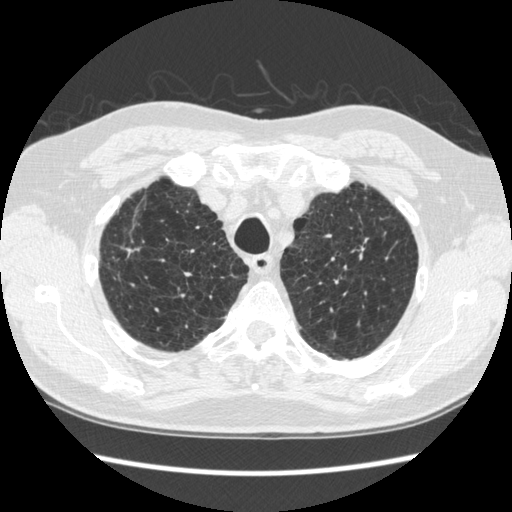
Axial slice from a low-dose chest CT screening exam. Second screening round (one year after baseline). Lung window (W 1500 / L -600 HU). 1.25 mm slice thickness. 120 kVp. 512 × 512 image matrix. Male, age 70 years at enrolment. Former smoker at enrolment.
- Lesion marked by an expert reader, bounding box <334,212,394,279> (left, top, right, bottom; pixels).
- The screening reader recorded 5 non-calcified nodules or masses ≥4 mm on this exam (right lower lobe, right lower lobe, right lower lobe, left upper lobe, left lower lobe); which of them this box marks is not recorded.
- Participant outcome: lung cancer diagnosed 479 days after this screen — squamous cell carcinoma, NOS, left upper lobe, moderately differentiated (G2), stage IA (AJCC 6th edition), 18 mm at pathology.